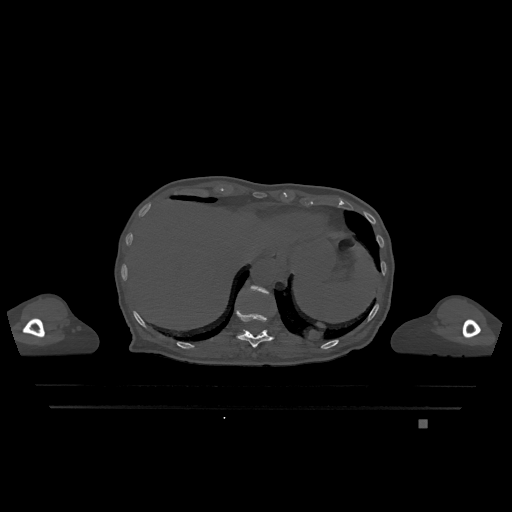
CT including the spine, one axial slice. Slice 577 of 1317 in the series (ordered by position). Bone window (W 1800 / L 400 HU). 512 × 512 image matrix, field of view 500 × 500 mm. Patient: female, 74 years. From the clinical record (not read from this slice): primary cancer: lung.
Structures marked on this image (semi-automatically segmented with operator editing):
- T11 vertebra: bounding box [x1, y1, x2, y2] px = [236, 308, 274, 348]
- T12 vertebra: [250, 286, 269, 294]